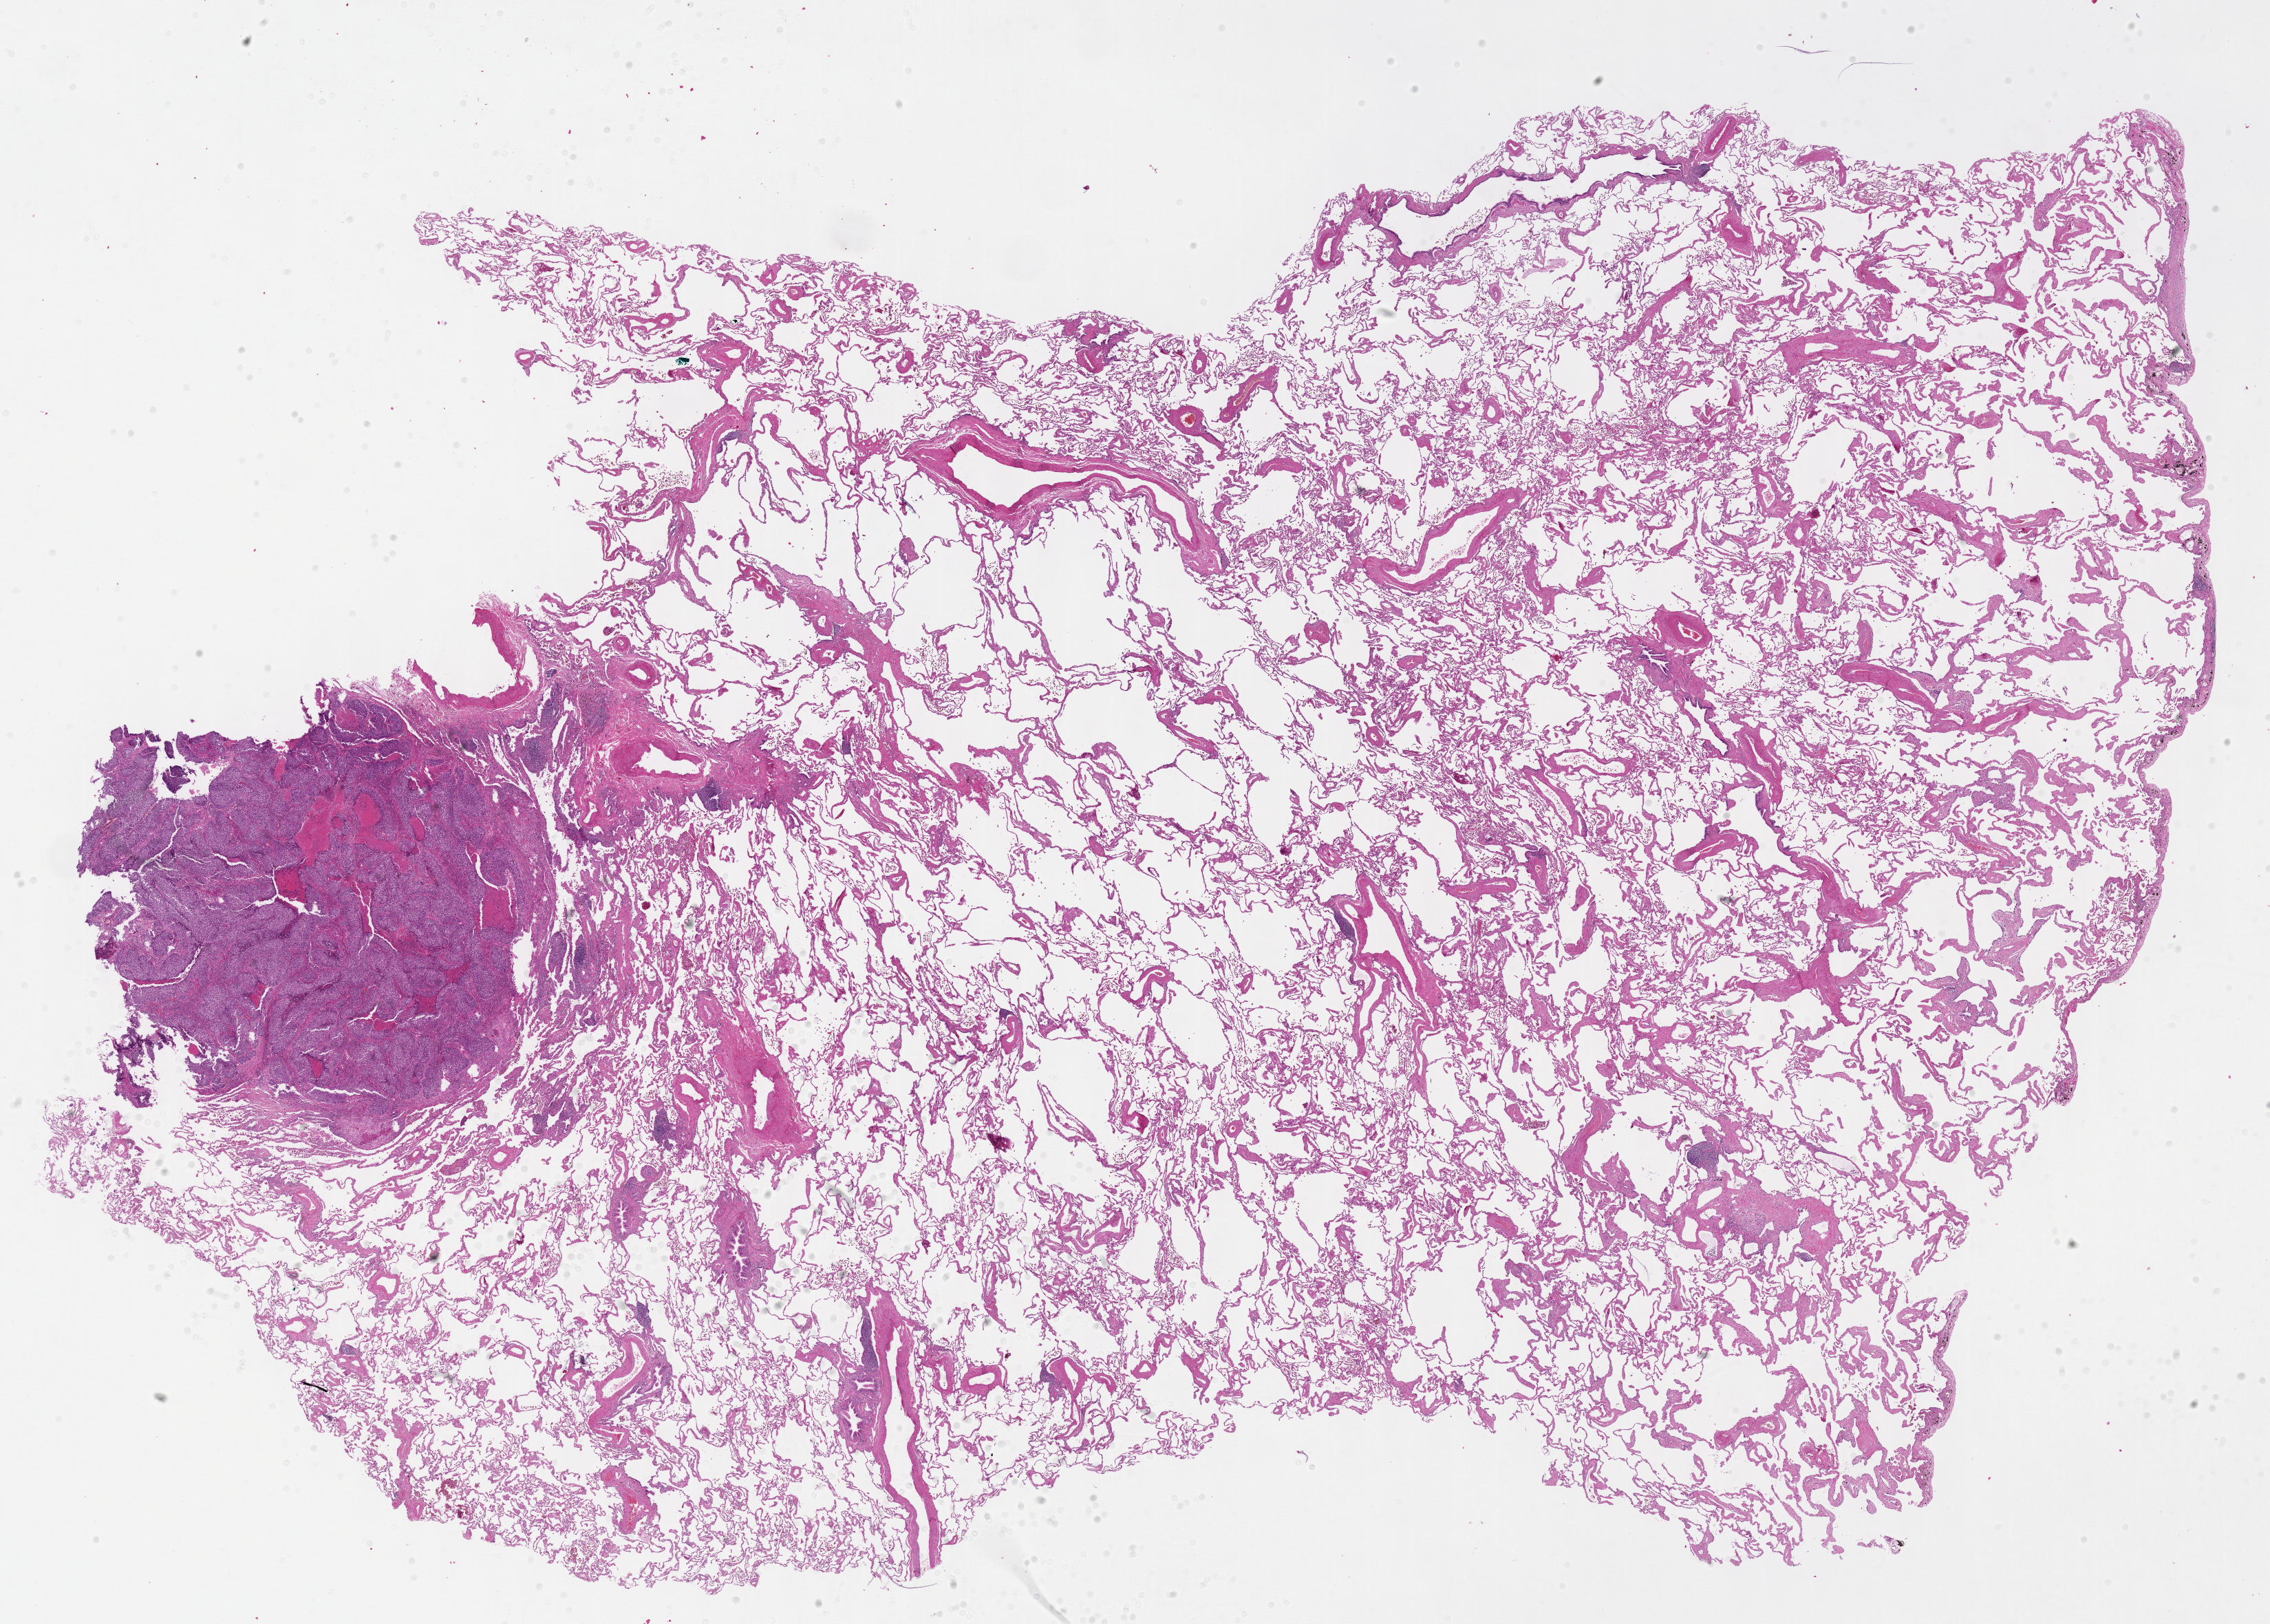
Digitized H&E tissue section (whole slide) — shown as a low-resolution overview of the whole scanned area (about 26.7 x 19.1 mm, acquisition: 40x scan), FFPE section, lung, primary tumour sample. Male patient; age at initial diagnosis 53 years.
Pathologic diagnosis: Basaloid squamous cell carcinoma (lower lobe, lung). TNM: T1 N0 M0. AJCC pathologic stage: IA (6th edition).